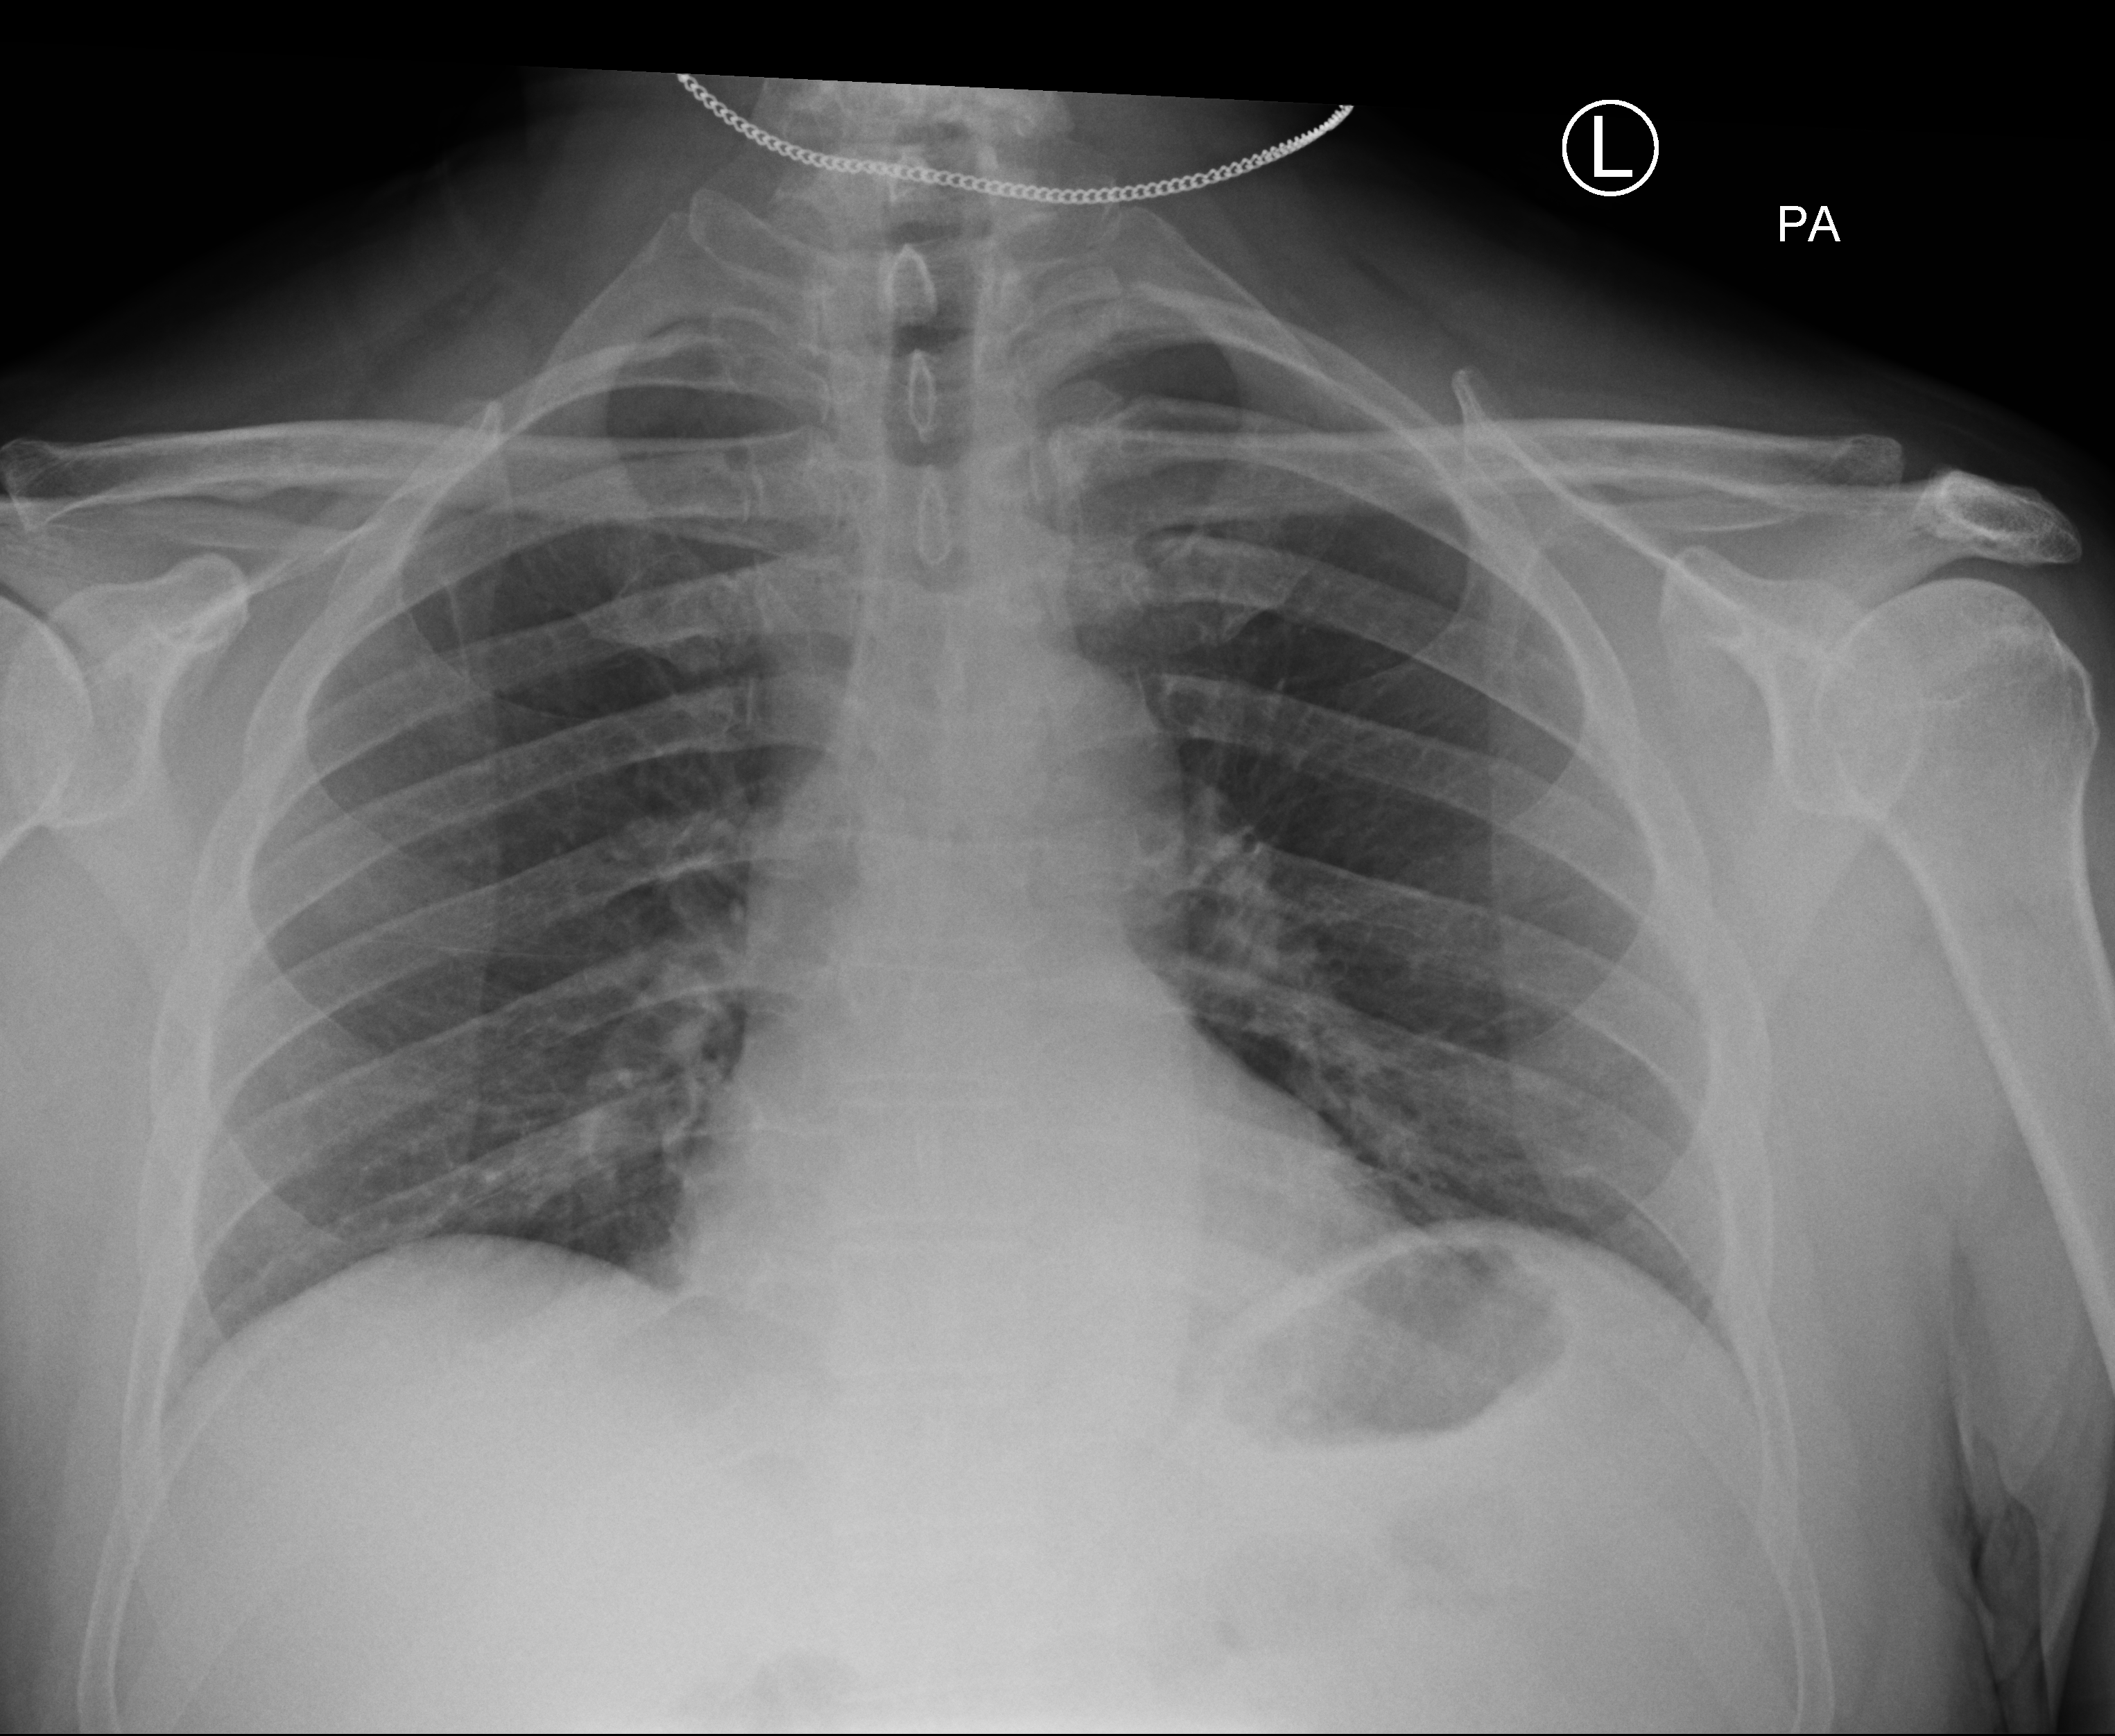
Bedside chest radiograph (computed radiography); anteroposterior (AP) projection. Male patient hospitalised with COVID-19, age 60–74 years.
Hospital-stay facts (about this admission, not read from this image; timing relative to this image not recorded): mechanically ventilated during this hospital stay: no.